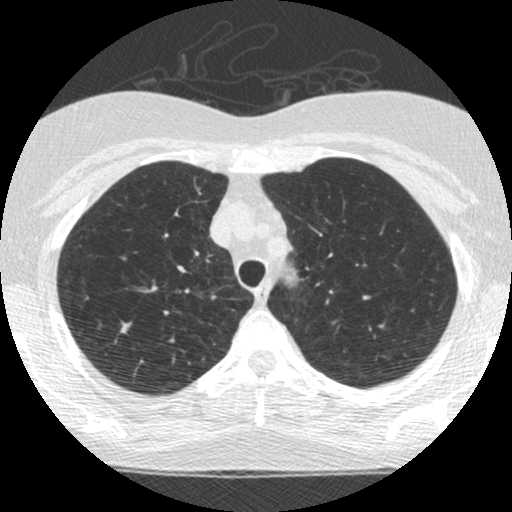
Low-dose screening chest CT, one axial slice. Reconstruction kernel STANDARD. Lung window (W 1500 / L -600 HU). 1.25 mm slice thickness. 512 × 512 image matrix, field of view 294 × 294 mm.
Annotated regions visible in this slice (outlined manually by an expert reader):
- lesion 1 (tumor, upper lobe of right lung): bounding box (x1, y1, x2, y2) in pixels: (120, 321, 132, 336)